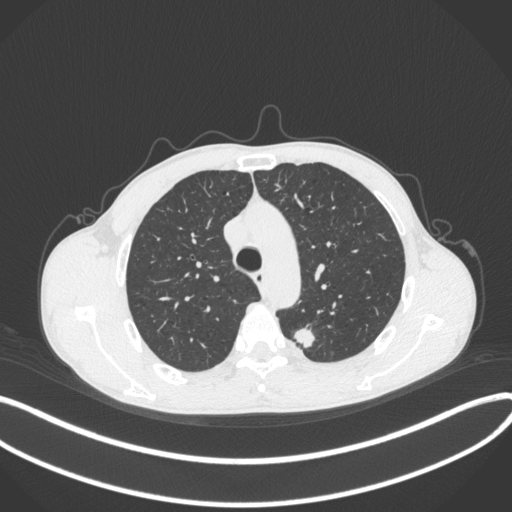
Chest CT, one axial slice. Position 294 of 429 along the scan axis. 120 kVp. Lung window (W 1500 / L -600 HU). 512 × 512 image matrix. Male patient, age 51 years. From the clinical record (not read from this slice): clinical TNM (as recorded): T2a N1 M1.
Annotated regions visible in this slice (bounding box drawn by a radiologist):
- lung tumour (recorded histology: adenocarcinoma): bounding box [x1, y1, x2, y2] px = [294, 325, 318, 350]